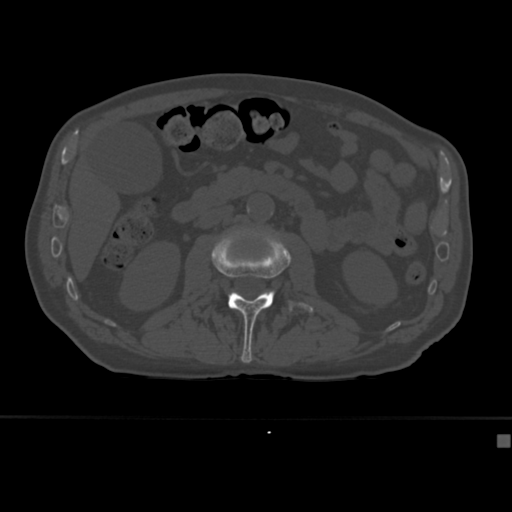
CT including the spine, one axial slice. Slice 145 of 430 in the series (ordered by position). Reconstruction kernel Br40s. Bone window (W 1800 / L 400 HU). 512 × 512 image matrix. Male patient, age 64 years. Case-level facts recorded for this patient, not image findings: primary cancer: uterus.
Annotated regions visible in this slice (semi-automatic segmentation, software-assisted and operator-edited):
- L2 vertebra: box from (x=211, y=228) to (x=314, y=363) px